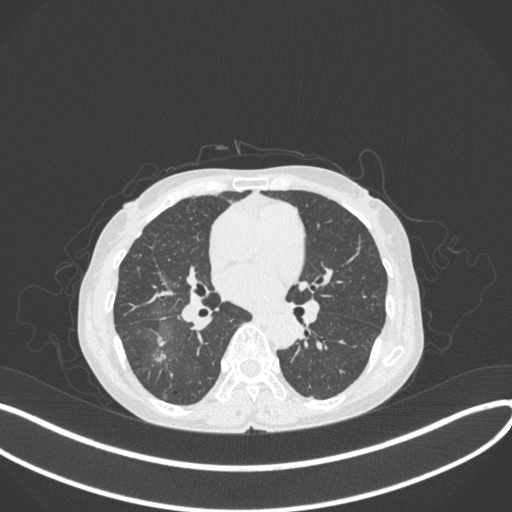
Chest CT, one axial slice. Slice 201 of 379 in the series (ordered by position). Reconstruction kernel B31f. Lung window (W 1500 / L -600 HU). 1 mm slice thickness. 512 × 512 image matrix. Female patient, age 69 years. From the clinical record (not read from this slice): clinical TNM (as recorded): T1b N0 M0.
Outlined on this slice (bounding box drawn by a radiologist):
- lung tumour (recorded histology: adenocarcinoma): bounding box (x1, y1, x2, y2) in pixels: (149, 331, 177, 367)